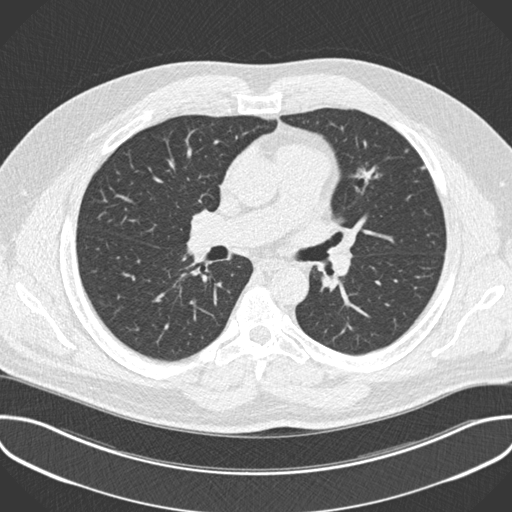
Low-dose screening chest CT, axial slice, first (baseline) screen, lung window (W 1500 / L -600 HU), 2 mm slice thickness, standard (soft-tissue) reconstruction kernel (B30f), 120 kVp, slice 78 of 201 in the series, 512 × 512 image matrix. Male participant, aged 55 years at enrolment. Former smoker at enrolment.
Expert reader's lesion annotation, bounding box [x1, y1, x2, y2] px = [341, 157, 392, 194]. The exam's reader record, not a measurement of the box and not confirmed to be the same lesion: non-calcified nodule or mass ≥4 mm, lingula, 13 × 12 mm, spiculated (stellate) margins, soft tissue attenuation. Official screen result: positive, change unspecified: nodule(s) >= 4 mm or enlarging nodule(s), mass(es), or other non-specific abnormalities suspicious for lung cancer.